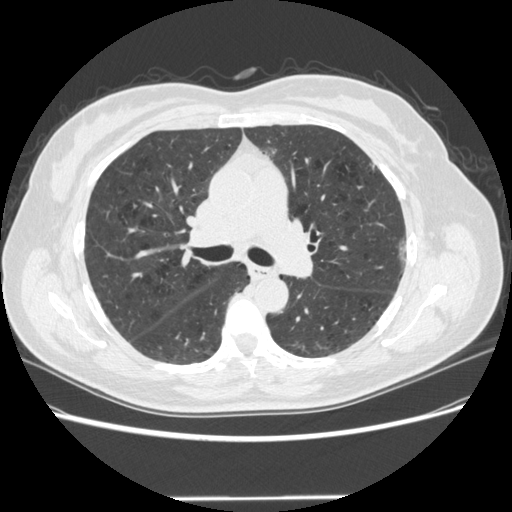
Low-dose screening chest CT, axial slice, baseline screening round, lung window (W 1500 / L -600 HU), 1.25 mm slice thickness, standard (soft-tissue) reconstruction kernel (STANDARD), 120 kVp, 512 × 512 image matrix, field of view 360 × 360 mm. Female, age 61 years at enrolment.
Expert reader's lesion annotation, bounding box (x1, y1, x2, y2) in pixels: (382, 226, 425, 277). No non-calcified nodule or mass ≥4 mm was recorded by the screening reader at this exam. Official screen result: negative screen, minor abnormalities not suspicious for lung cancer. Lung cancer was diagnosed 791 days after this screen (after the second annual screen): bronchiolo-alveolar adenocarcinoma, NOS, left upper lobe, well differentiated (G1), stage IA (AJCC 6th edition), 11 mm at pathology.